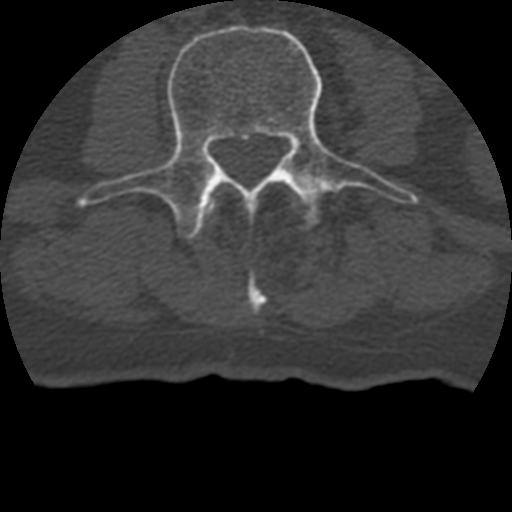
CT including the spine, one axial slice. Bone window (W 1800 / L 400 HU). 1.25 mm slice thickness. 512 × 512 image matrix, field of view 160 × 160 mm. Patient age 69 years. From the clinical record (not read from this slice): primary cancer: prostate.
Structures marked on this image (semi-automatic segmentation, software-assisted and operator-edited):
- L2 vertebra: bounding box (x1, y1, x2, y2) in pixels: (248, 284, 266, 313)
- L3 vertebra: (77, 24, 413, 239)